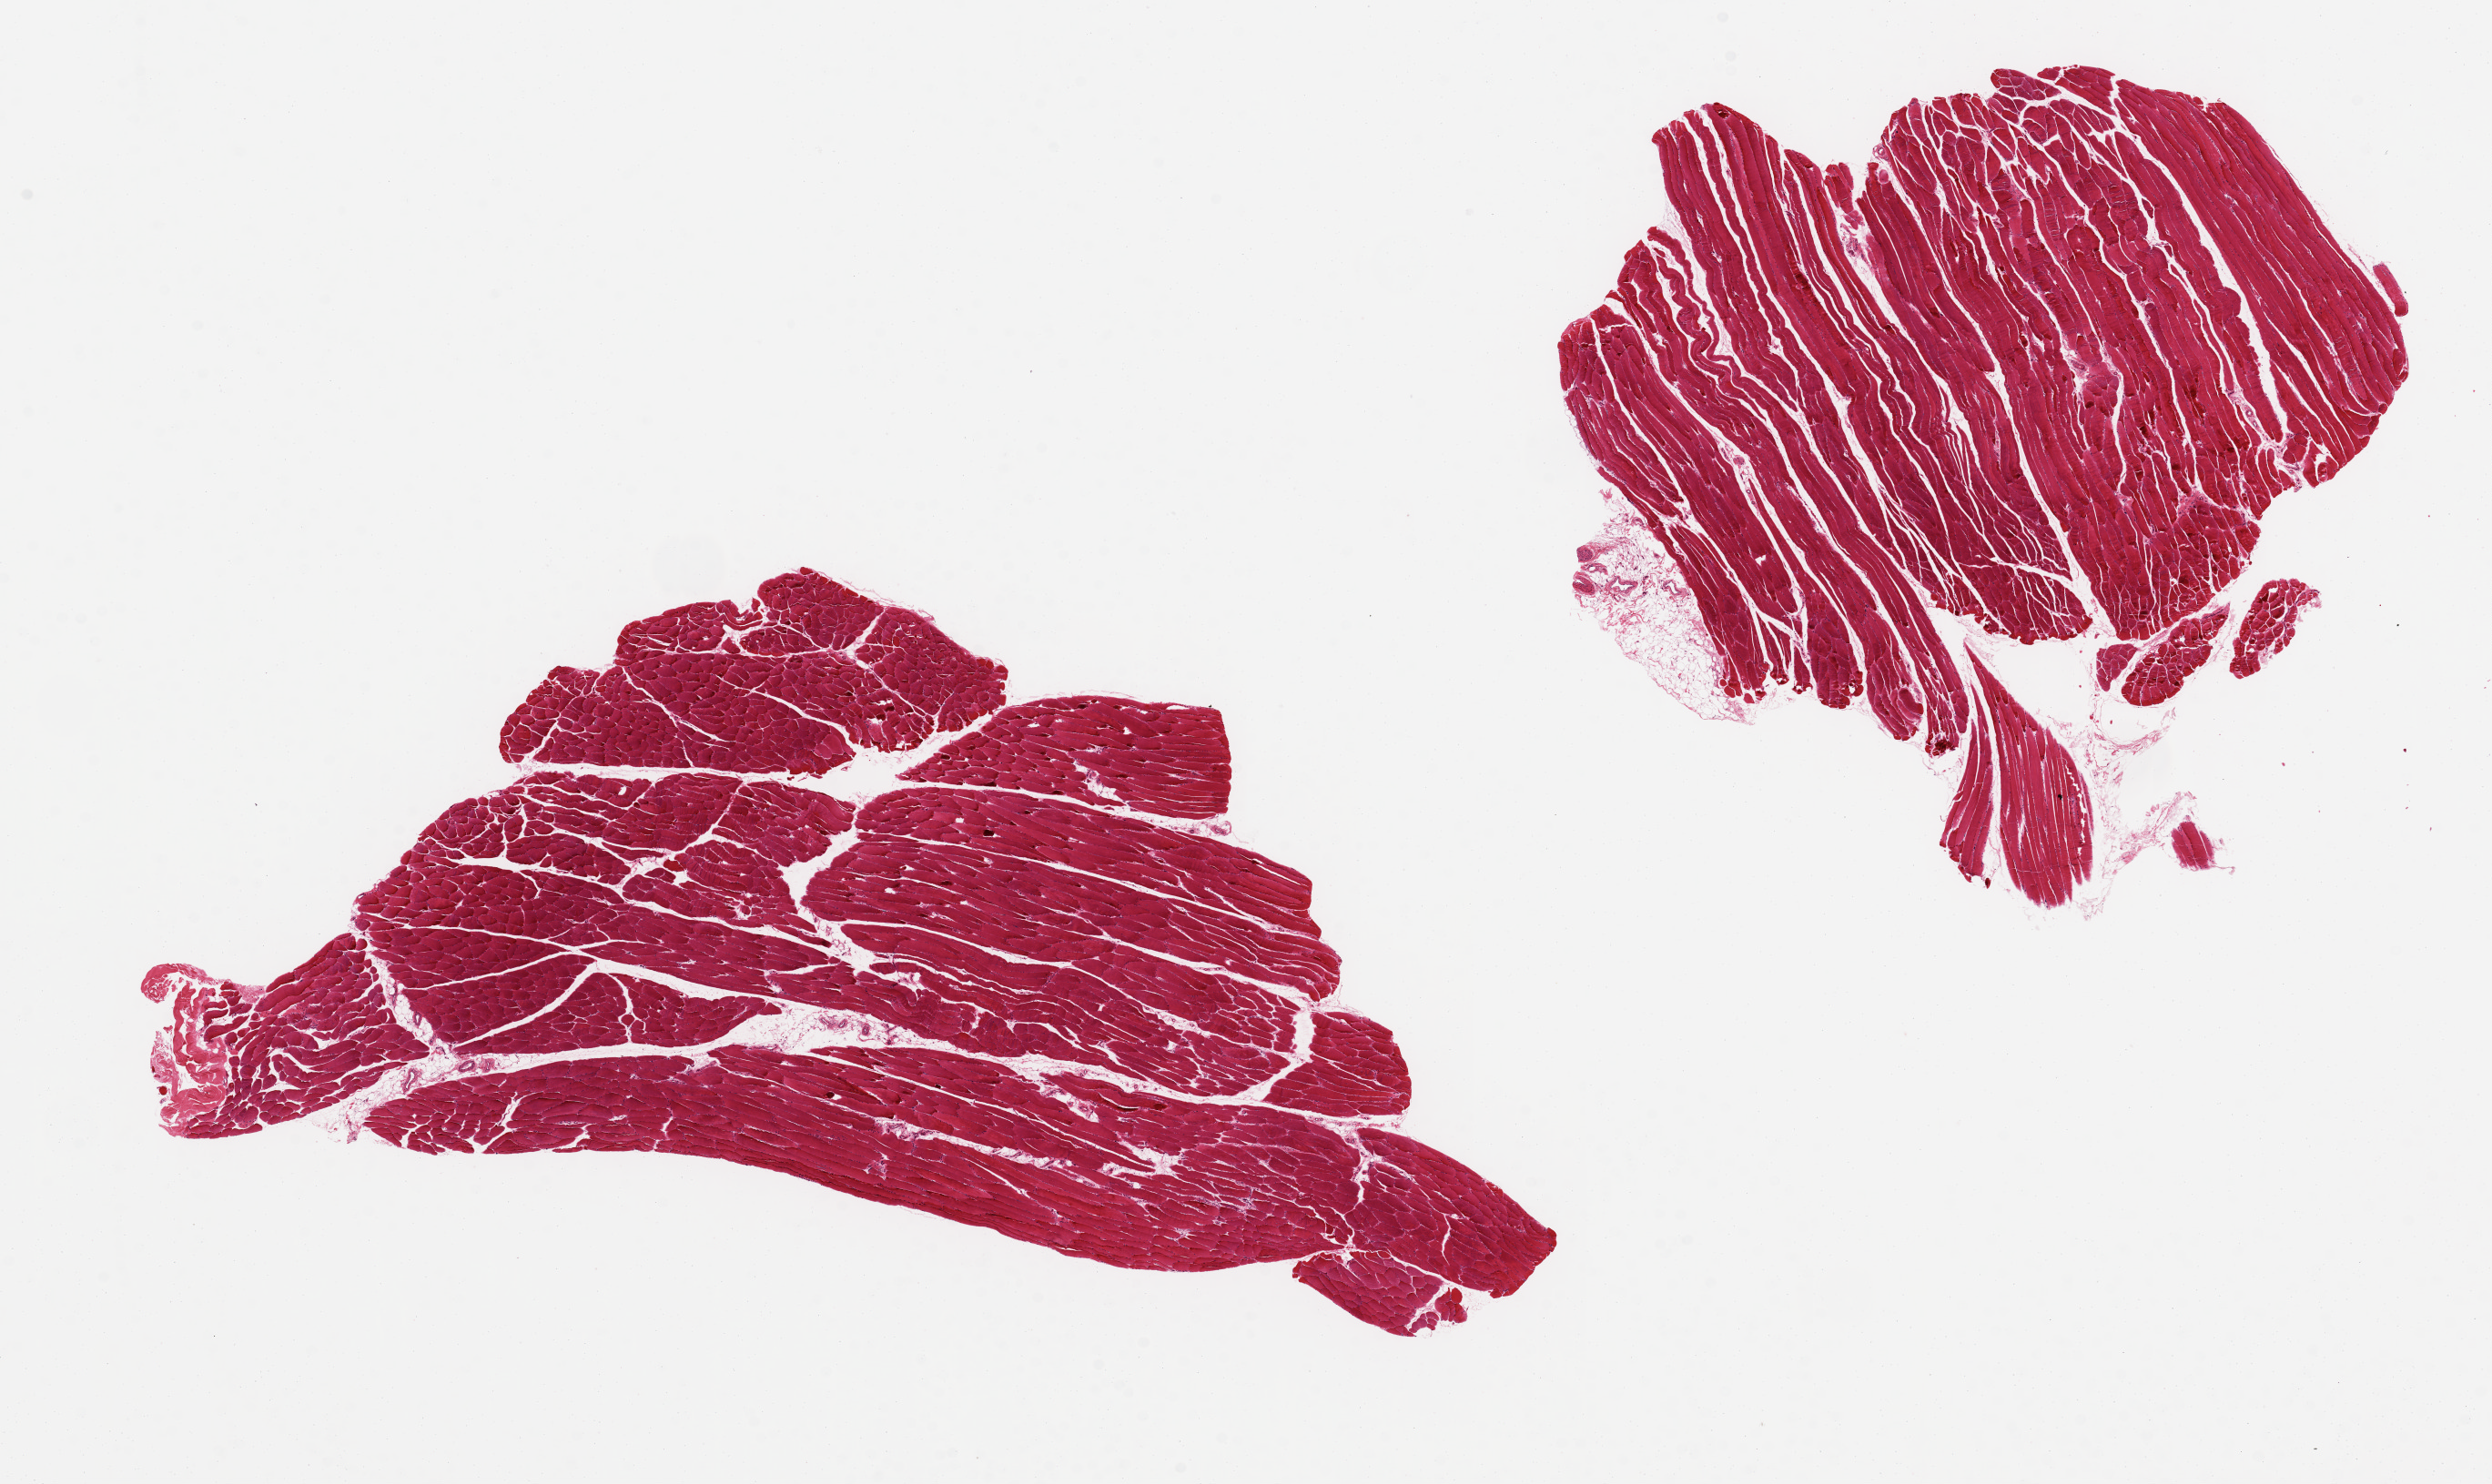
Digitized H&E-stained section, brightfield, whole scanned area (about 21.7 x 12.9 mm) shown as a low-resolution overview. PAXgene-fixed paraffin-embedded (PFPE) section. Section of skeletal muscle (target tissue). Donor tissue sample.
- review note (as recorded): 2 pieces 9x5 & 7x6 mm; minimal adipose